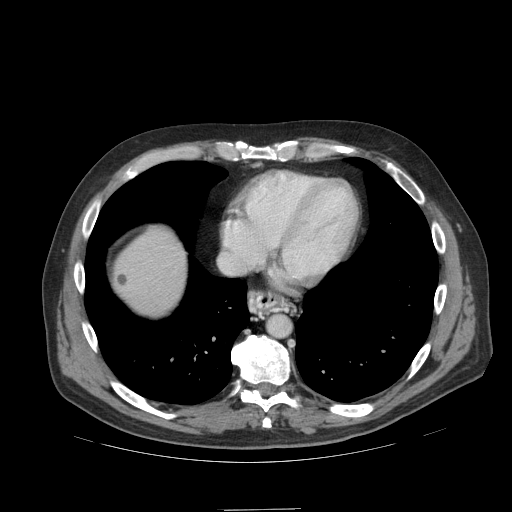
Contrast-enhanced abdominal CT (liver protocol), one axial slice. Position 94 of 99 along the scan axis. Reconstruction kernel STANDARD. 140 kVp. Soft-tissue window (W 400 / L 40 HU). 2.5 mm slice thickness. 512 × 512 image matrix, field of view 440 × 440 mm. Case-level facts recorded for this patient, not image findings: diagnosis: hepatocellular carcinoma (patient treated with transarterial chemoembolisation; whether this scan precedes or follows treatment is not stated here); TNM stage (as recorded): Stage-I; Child-Pugh class: A; tumour differentiation: no biopsy; tumour nodularity: uninodular.
Annotated regions visible in this slice (semi-automatic segmentation, software-assisted and operator-edited):
- abdominal aorta: box from (x=267, y=315) to (x=290, y=337) px
- liver parenchyma outside the tumour (the mass and vessels are separate outlines, so this box may not span the whole liver): (x=114, y=228)–(x=186, y=314)